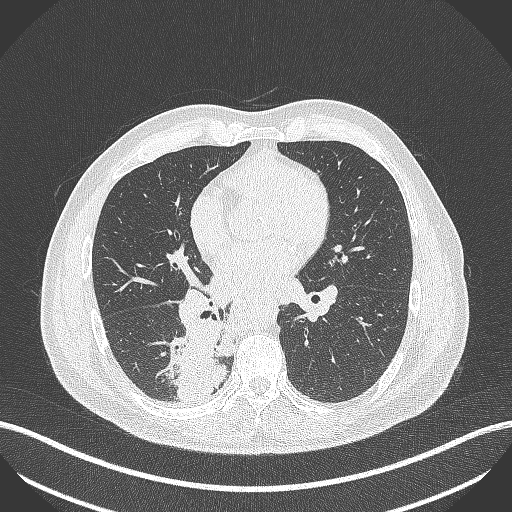
Chest CT, one axial slice; position 225 of 451 along the scan axis; 100 kVp; lung window (W 1500 / L -600 HU); 1 mm slice thickness; 512 × 512 image matrix, field of view 400 × 400 mm. Male patient, age 61 years. From the clinical record (not read from this slice): clinical TNM (as recorded): T1 N0 M0.
Outlined on this slice (rectangle marked by the reading radiologist):
- lung tumour (recorded histology: small cell carcinoma): bounding box (x1, y1, x2, y2) in pixels: (175, 311, 230, 403)